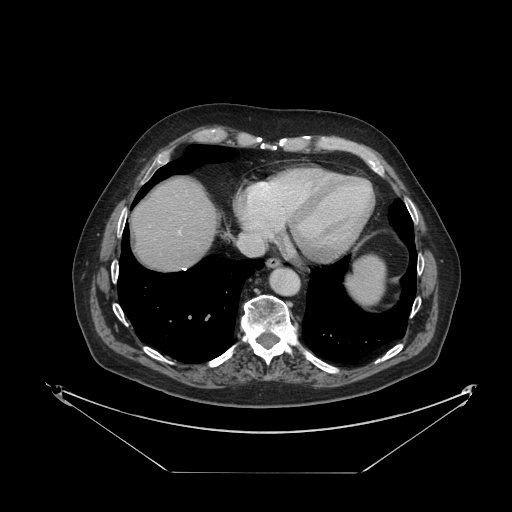
Contrast-enhanced abdominal CT, one axial slice. Position 112 of 121 along the scan axis. Reconstruction kernel STANDARD. 120 kVp. Intravenous contrast given. Soft-tissue window (W 400 / L 40 HU). 512 × 512 image matrix, field of view 500 × 500 mm. Male patient, age 68 years. From the clinical record (not read from this slice): diagnosis: colorectal cancer liver metastases, imaged before liver resection; multiple liver metastases: no; largest metastasis: 4 cm; chemotherapy before resection: yes.
Outlined on this slice (manually delineated by an expert):
- liver: box from (x=133, y=179) to (x=217, y=270) px
- planned liver remnant (the part of the liver to remain after resection): (x=133, y=179)–(x=217, y=270)